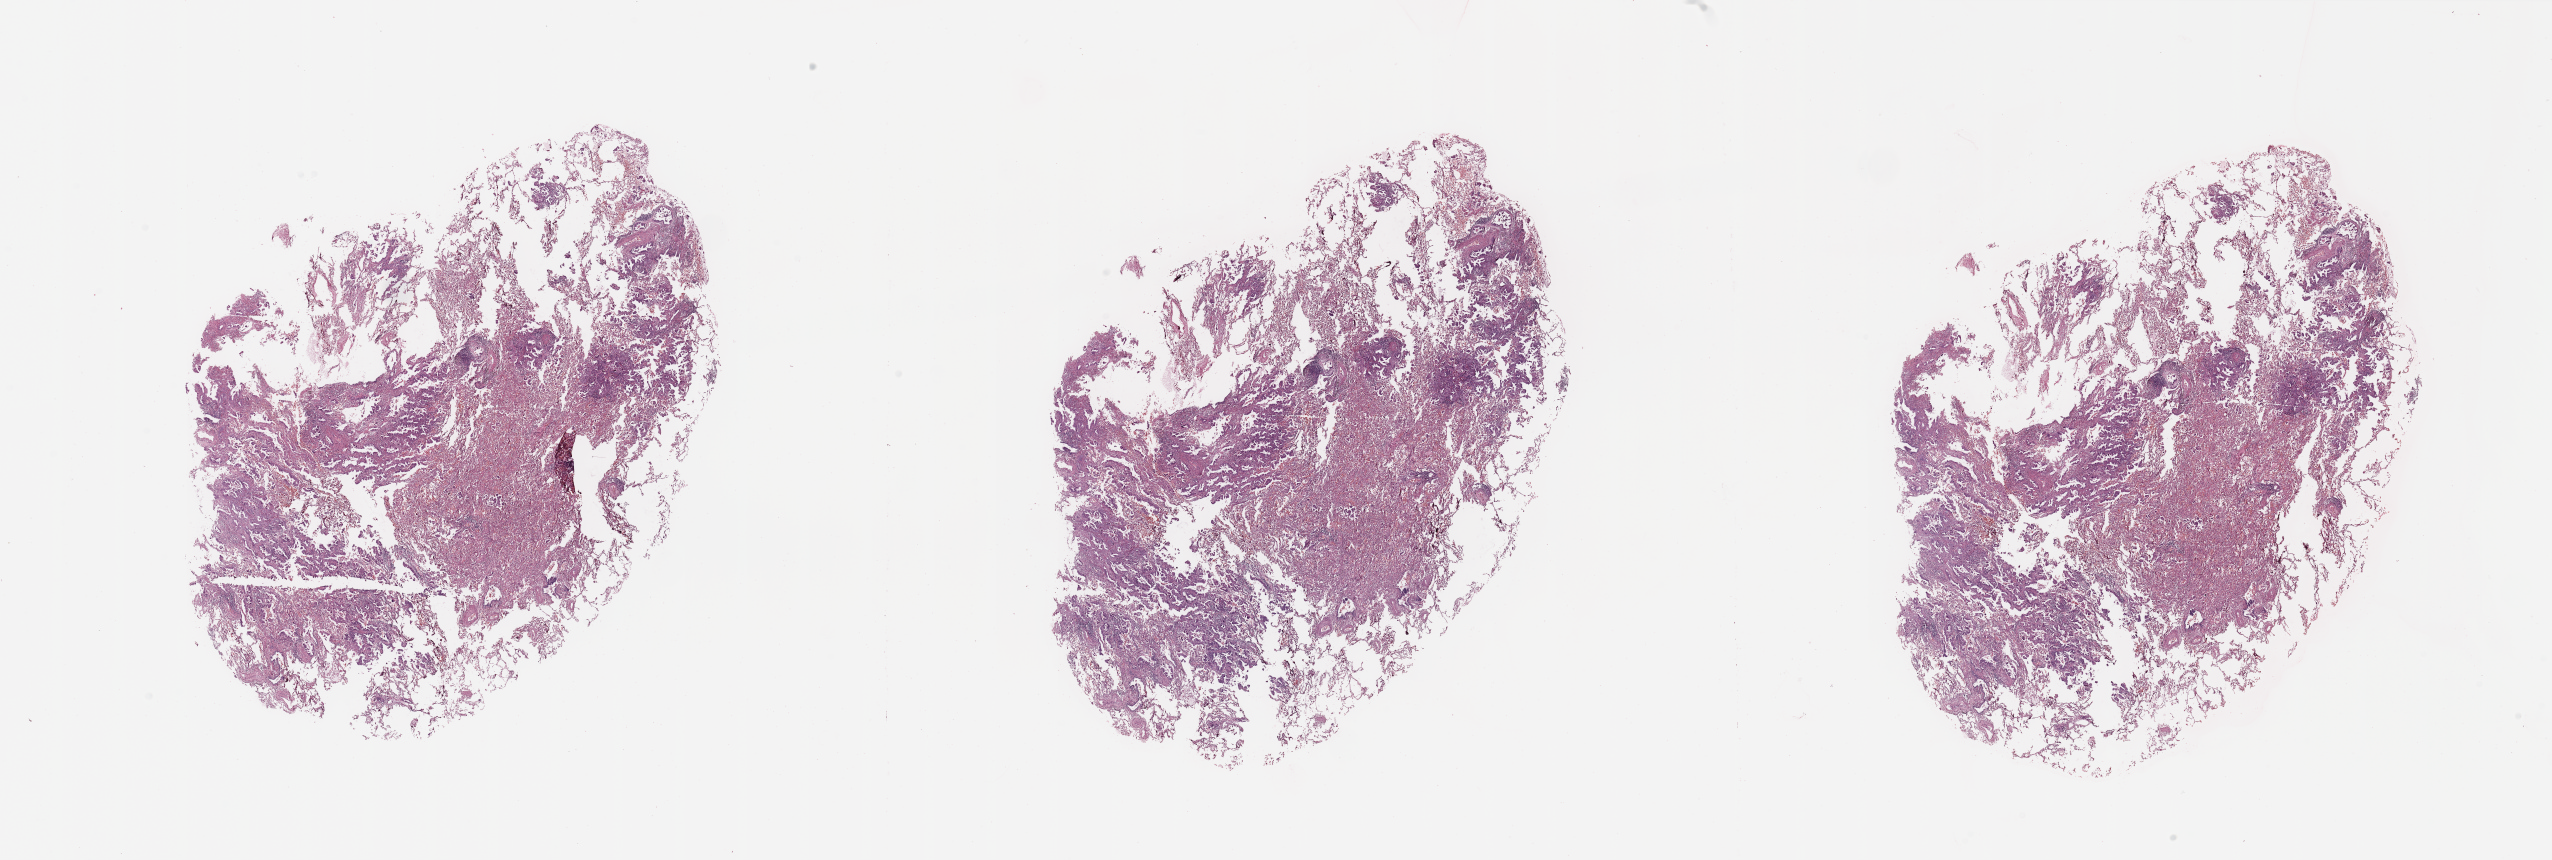
Hematoxylin and eosin (H&E) stained whole-slide image — a low-resolution overview of the entire scanned area, about 40.4 x 13.6 mm; lung, normal (non-tumour) tissue. 73-year-old female patient.
* this section: normal (non-tumour) tissue from the same patient
* patient diagnosis: Adenocarcinoma, NOS